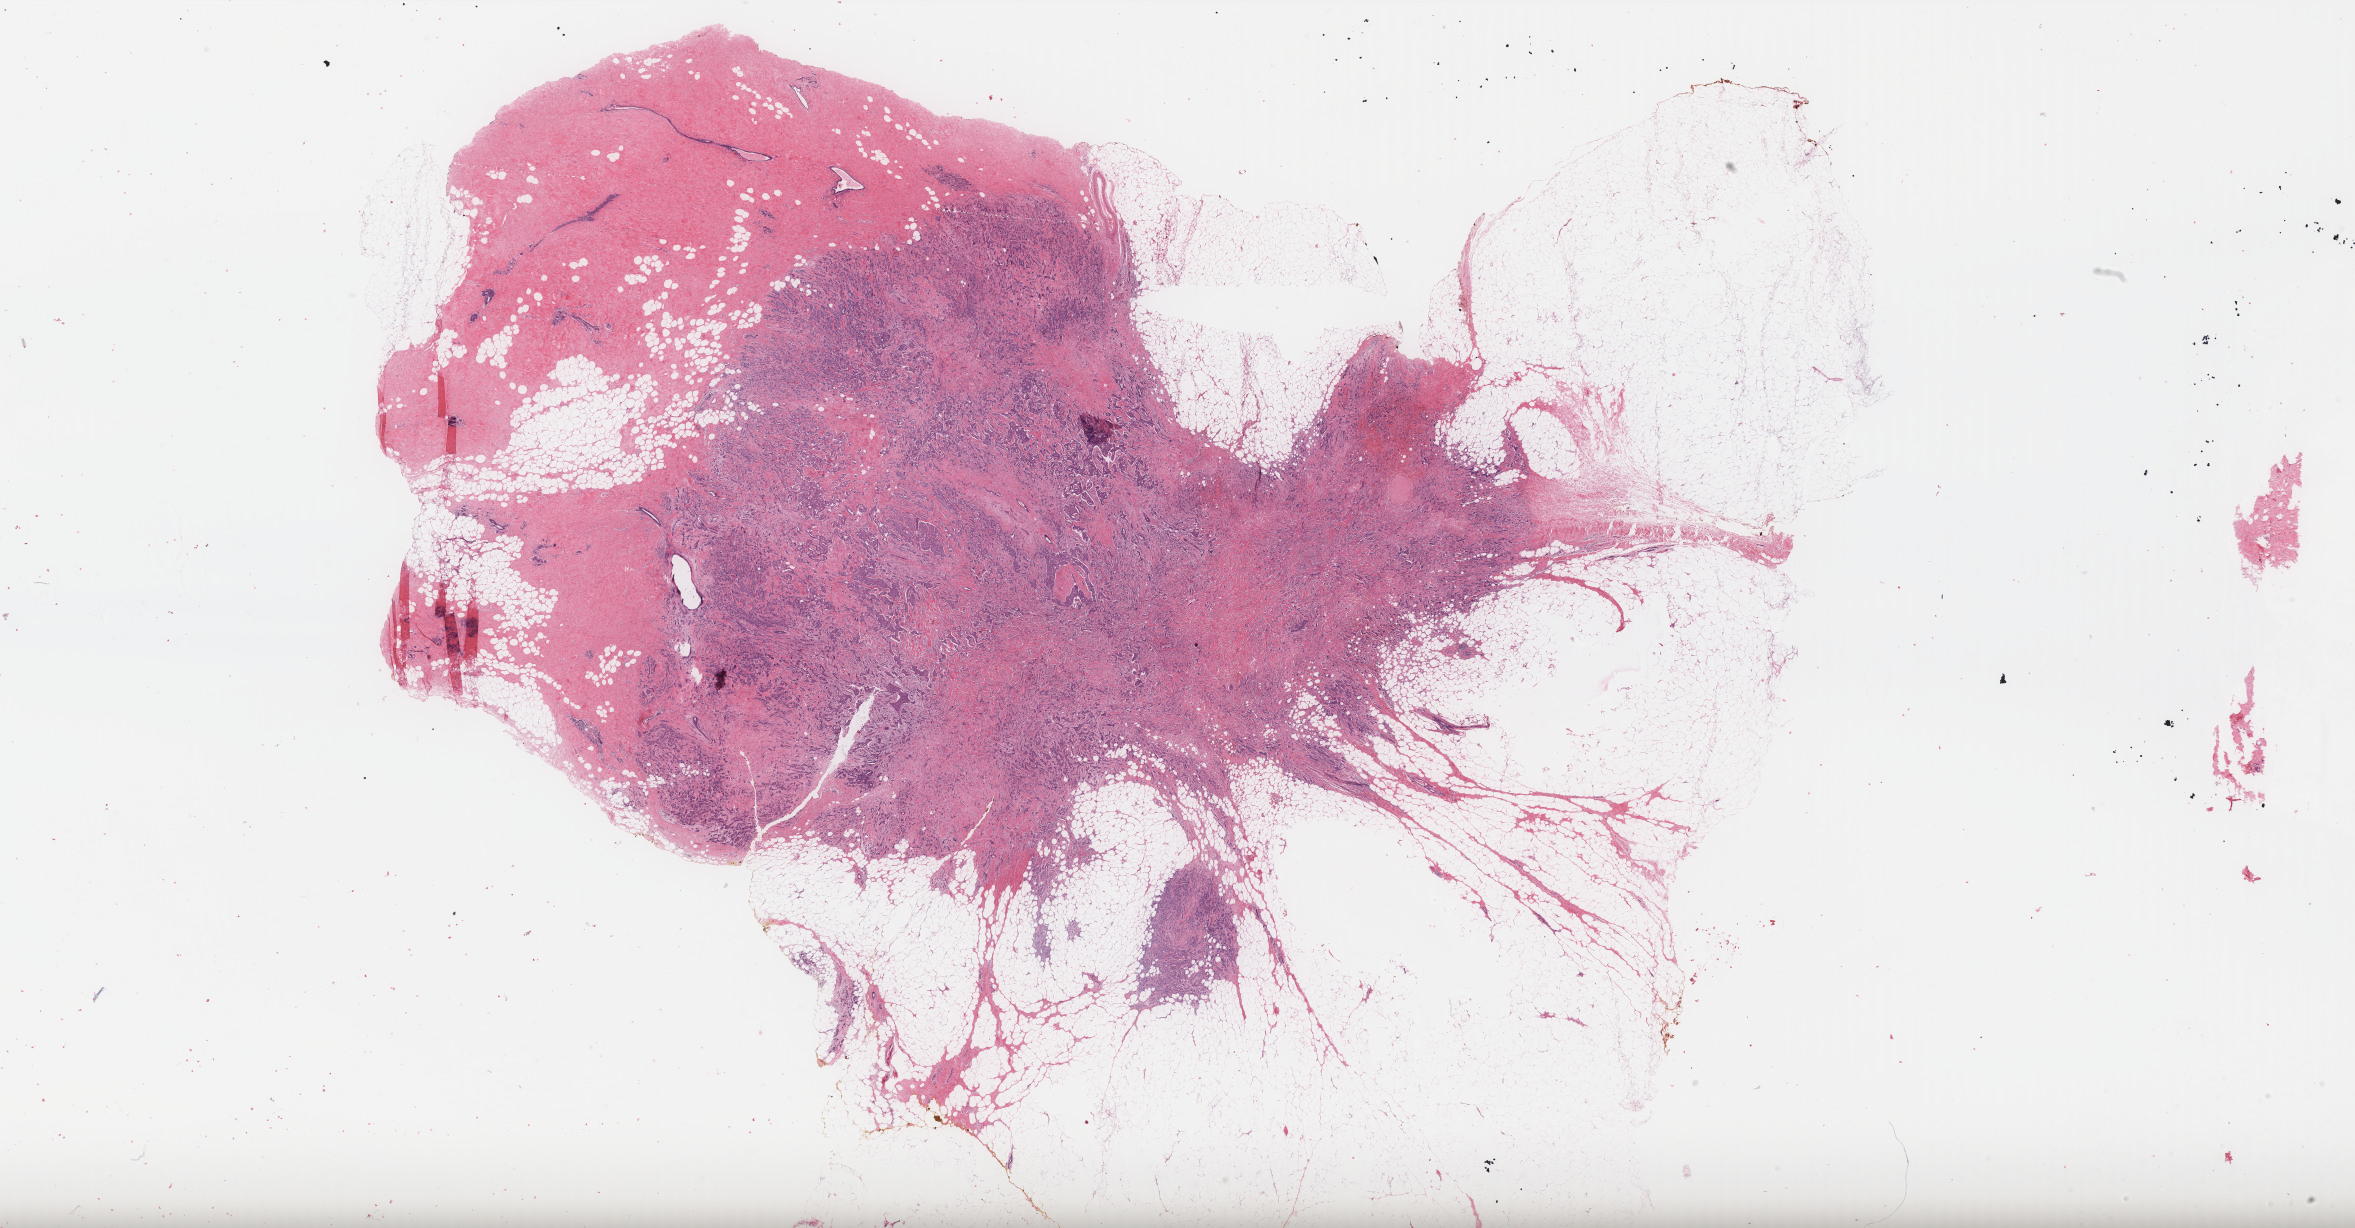
Digitized H&E tissue section (whole slide) — low-resolution overview of the scanned area, about 37.8 x 19.7 mm (acquisition: 40x scan). FFPE section. Sample: primary tumour, breast. Female, age 59 years at initial diagnosis.
- AJCC pathologic stage: IIB
- laterality: right
- lymph nodes positive (case pathology): 1 of 3 examined
- diagnosis: Infiltrating duct carcinoma, NOS